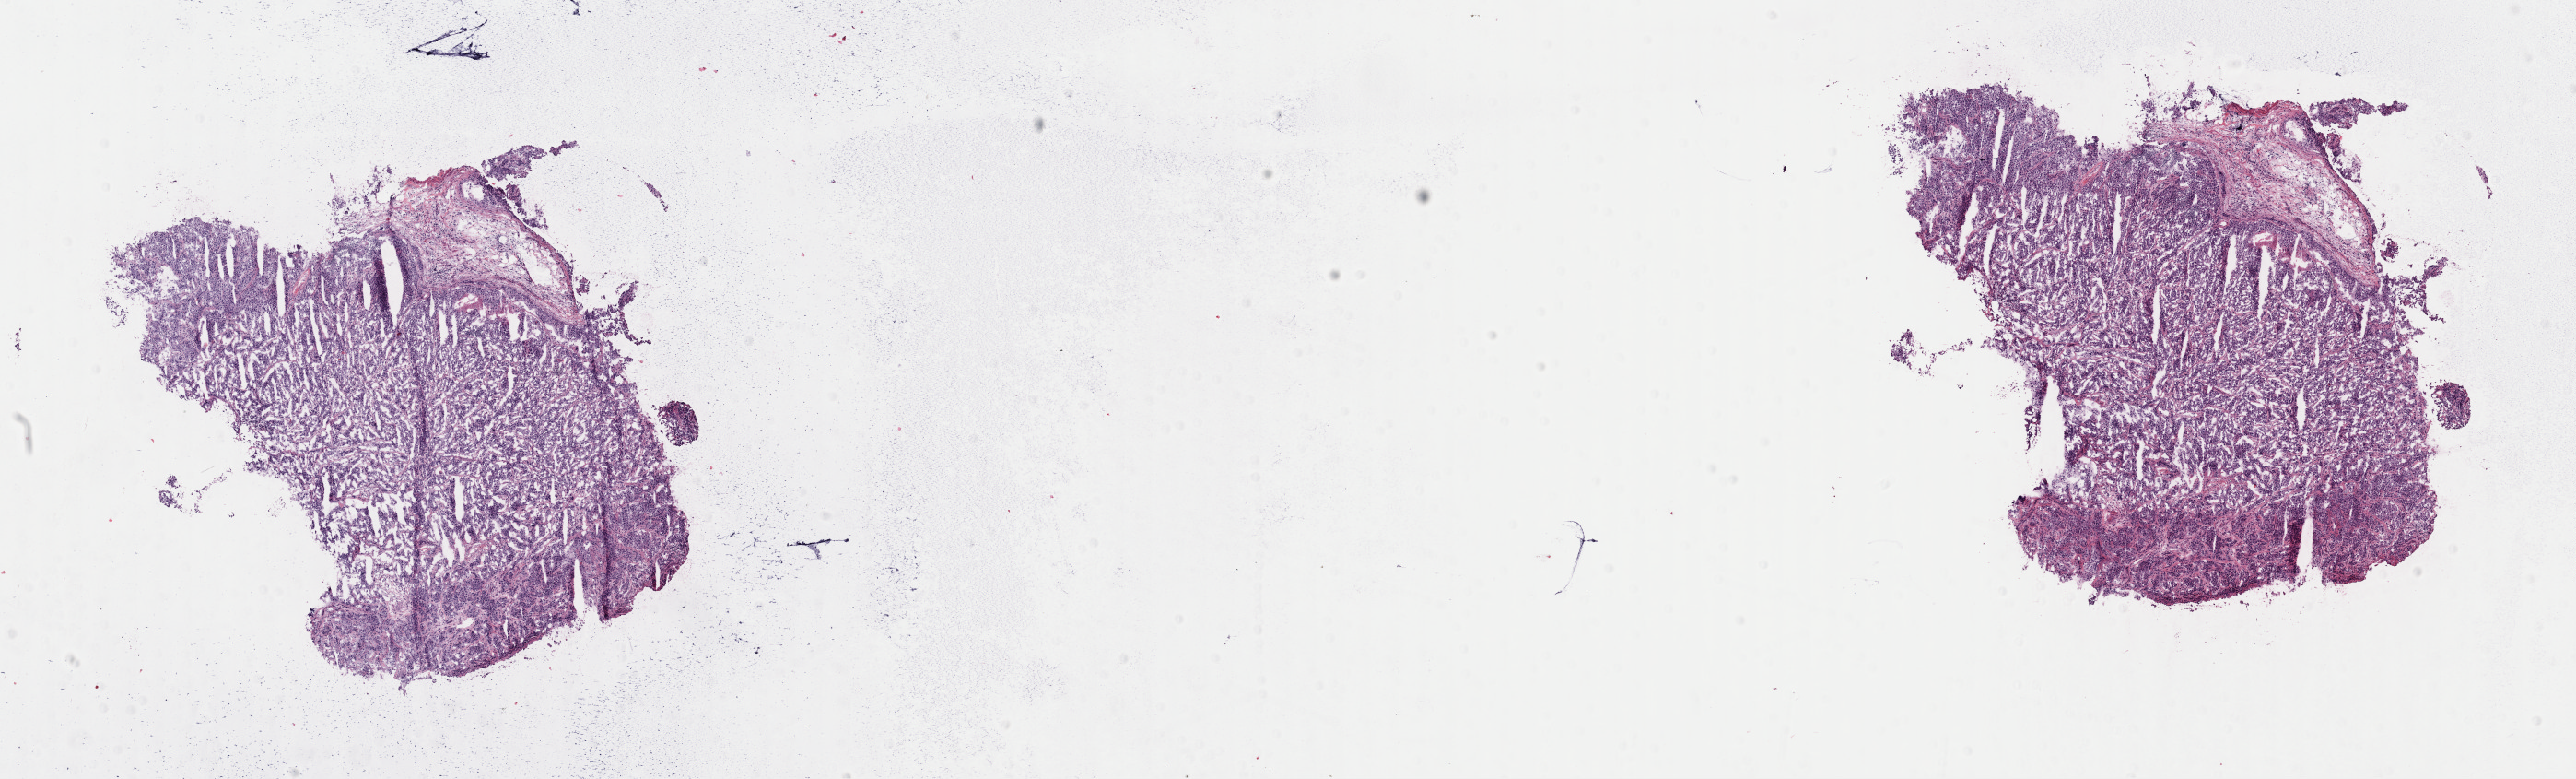
Whole-slide histology image, H&E-stained — shown as a low-resolution overview of the whole scanned area (about 22.1 x 6.7 mm); frozen section from the top of the tissue portion; sample: primary tumour, breast. Patient: female, age at initial diagnosis 36 years.
Pathologic diagnosis: Infiltrating duct carcinoma, NOS.